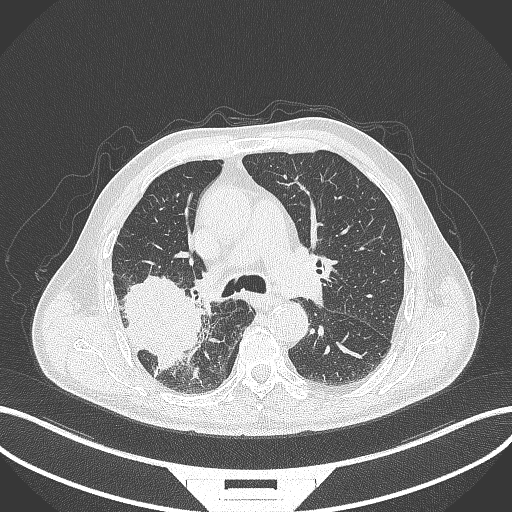
Chest CT, one axial slice; slice 258 of 429 in the series (ordered by position); reconstruction kernel B70f; 120 kVp; lung window (W 1500 / L -600 HU); 1 mm slice thickness; 512 × 512 image matrix. Patient: male, 72 years. Case-level facts recorded for this patient, not image findings: clinical TNM (as recorded): T3 N2 M0.
Outlined on this slice (bounding box drawn by a radiologist):
- lung tumour (recorded histology: adenocarcinoma): box from (x=118, y=272) to (x=205, y=375) px